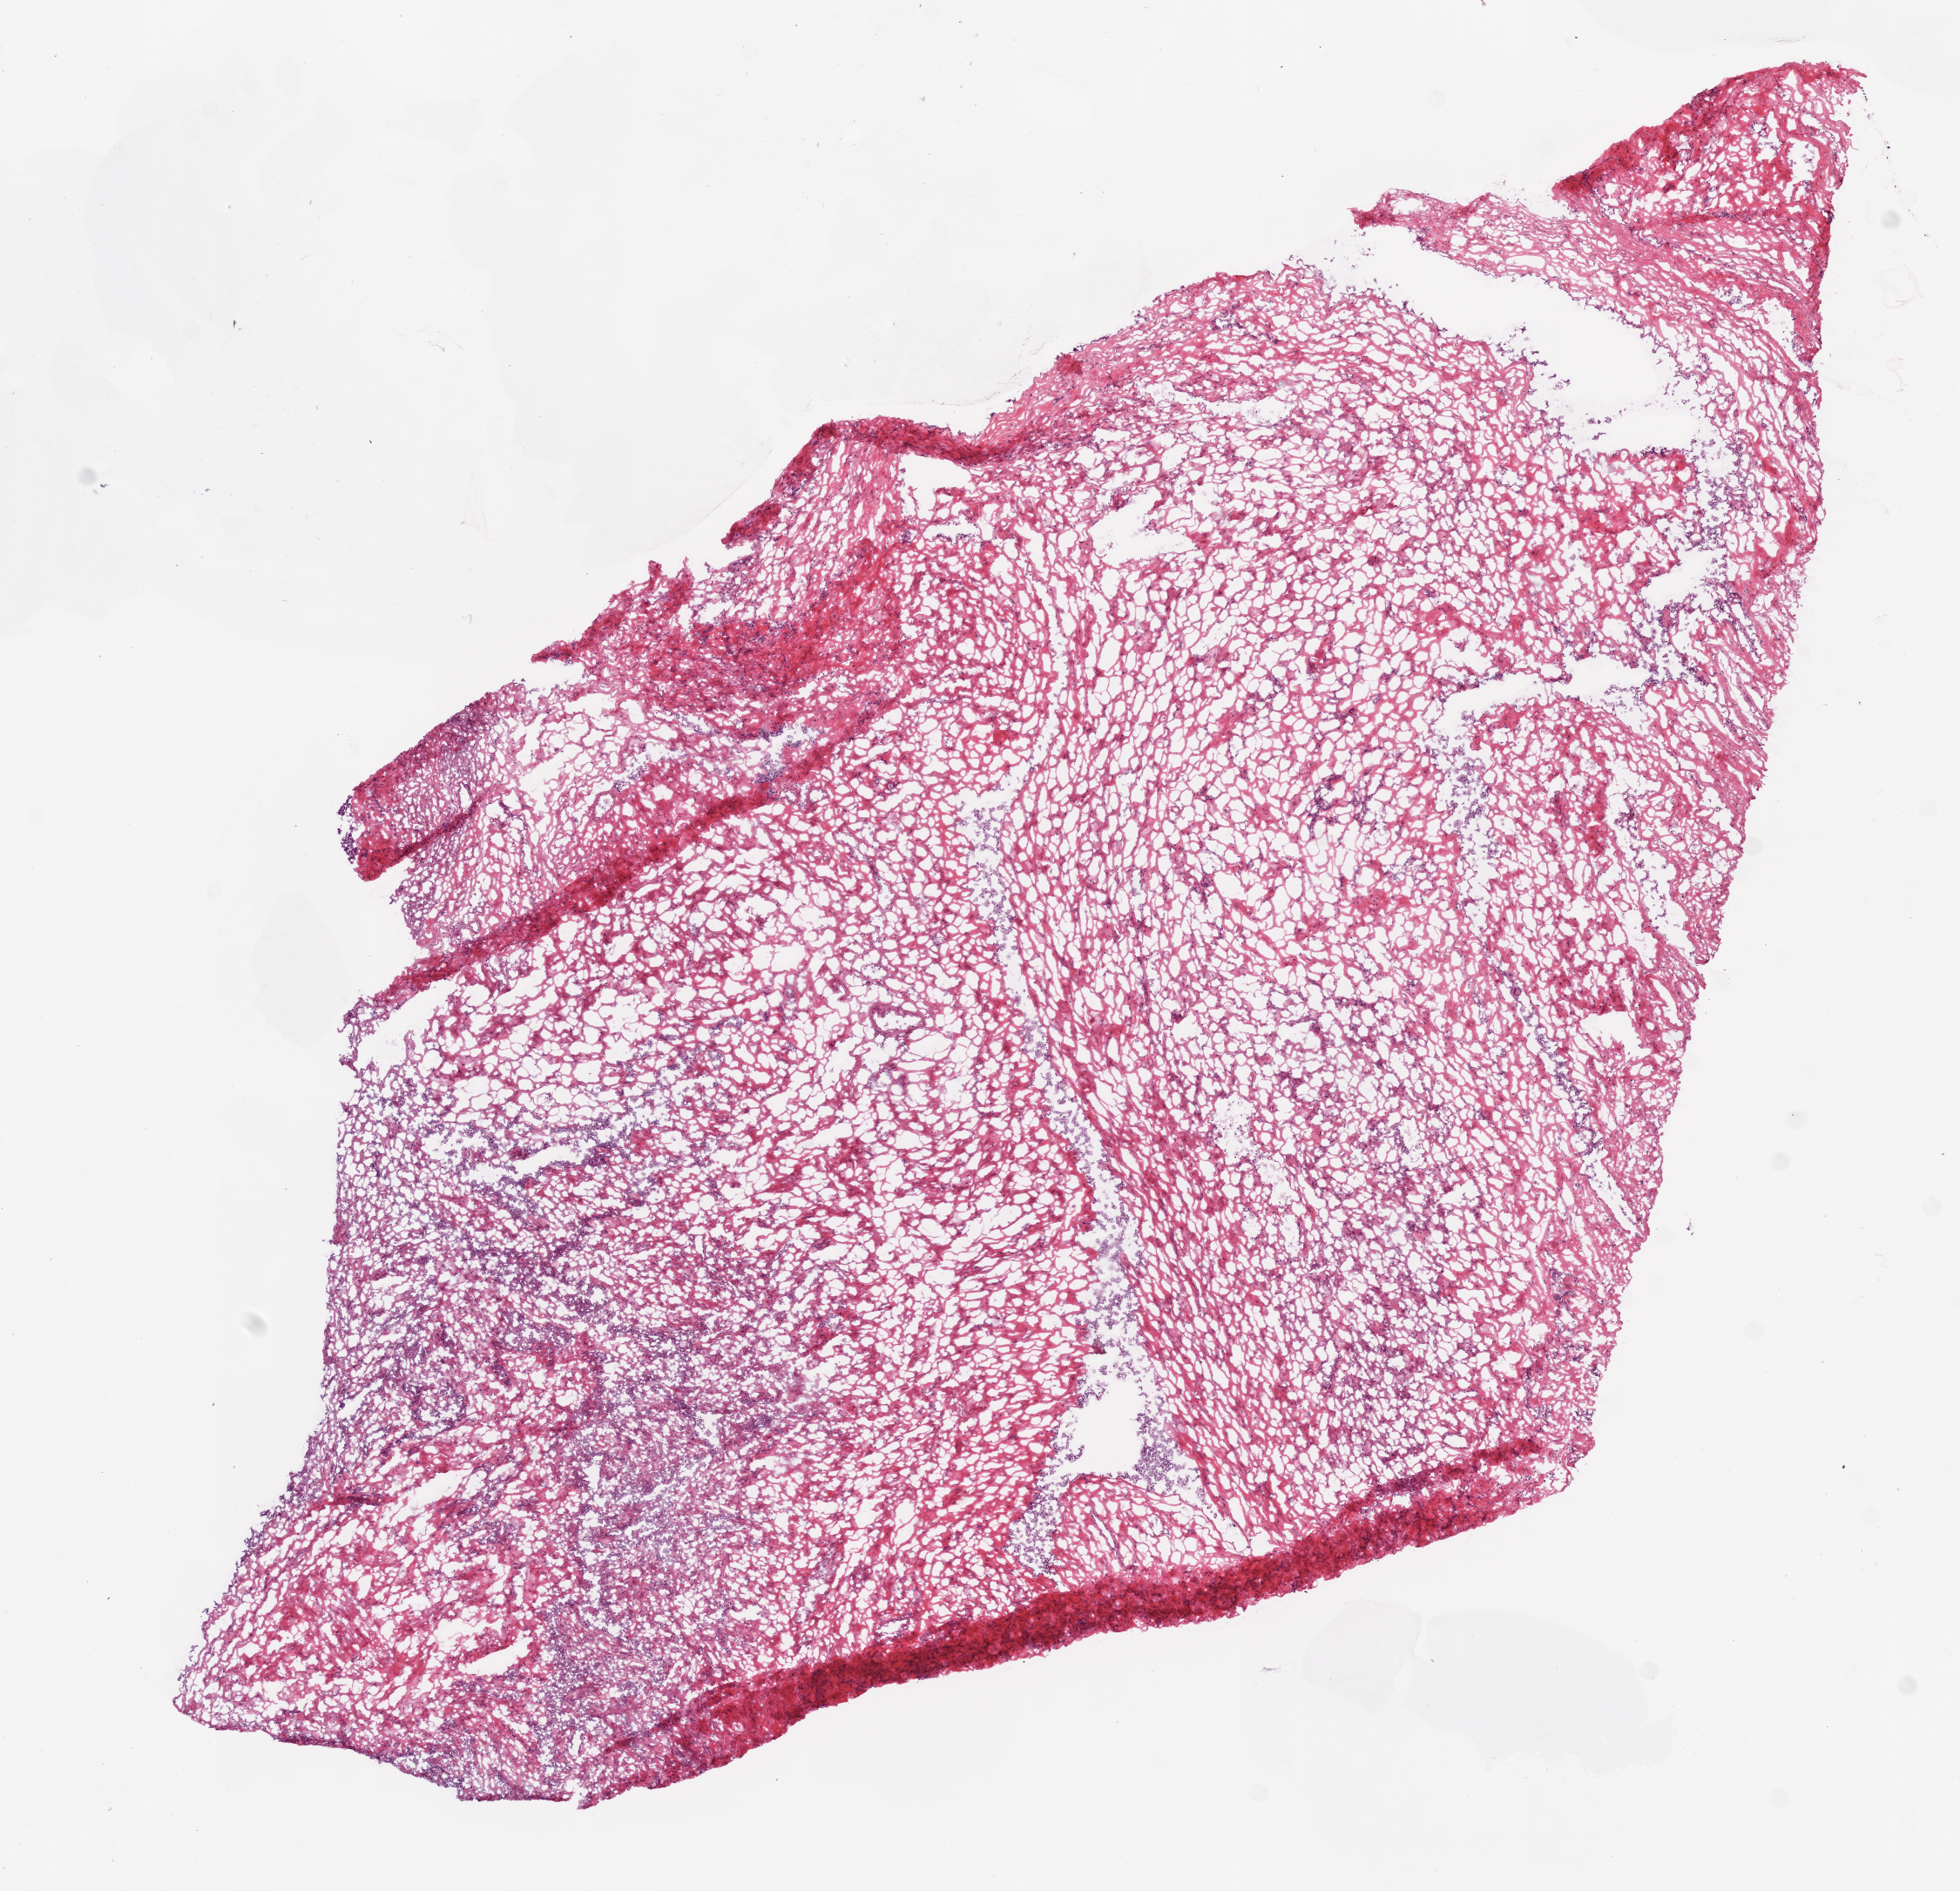
H&E whole-slide image, low-resolution overview of the scanned area, about 9.0 x 8.7 mm. Frozen section. Solid tissue normal (non-tumour tissue) sample from the ovary. Female patient; age at initial diagnosis 76 years.
- this section: solid tissue normal (non-tumour) sample from the same patient
- patient diagnosis: Serous cystadenocarcinoma, NOS